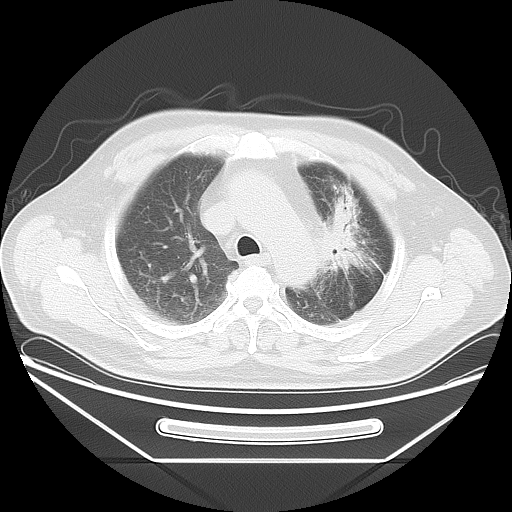
Chest CT, one axial slice; slice 29 of 37 in the series (ordered by position); reconstruction kernel LUNG; 120 kVp; lung window (W 1500 / L -600 HU); 512 × 512 image matrix. Patient: male, 61 years. Case-level facts recorded for this patient, not image findings: clinical TNM (as recorded): T2a N0 M0.
Annotated regions visible in this slice (bounding box drawn by a radiologist):
- lung tumour (recorded histology: small cell carcinoma): bounding box [x1, y1, x2, y2] px = [319, 177, 391, 301]